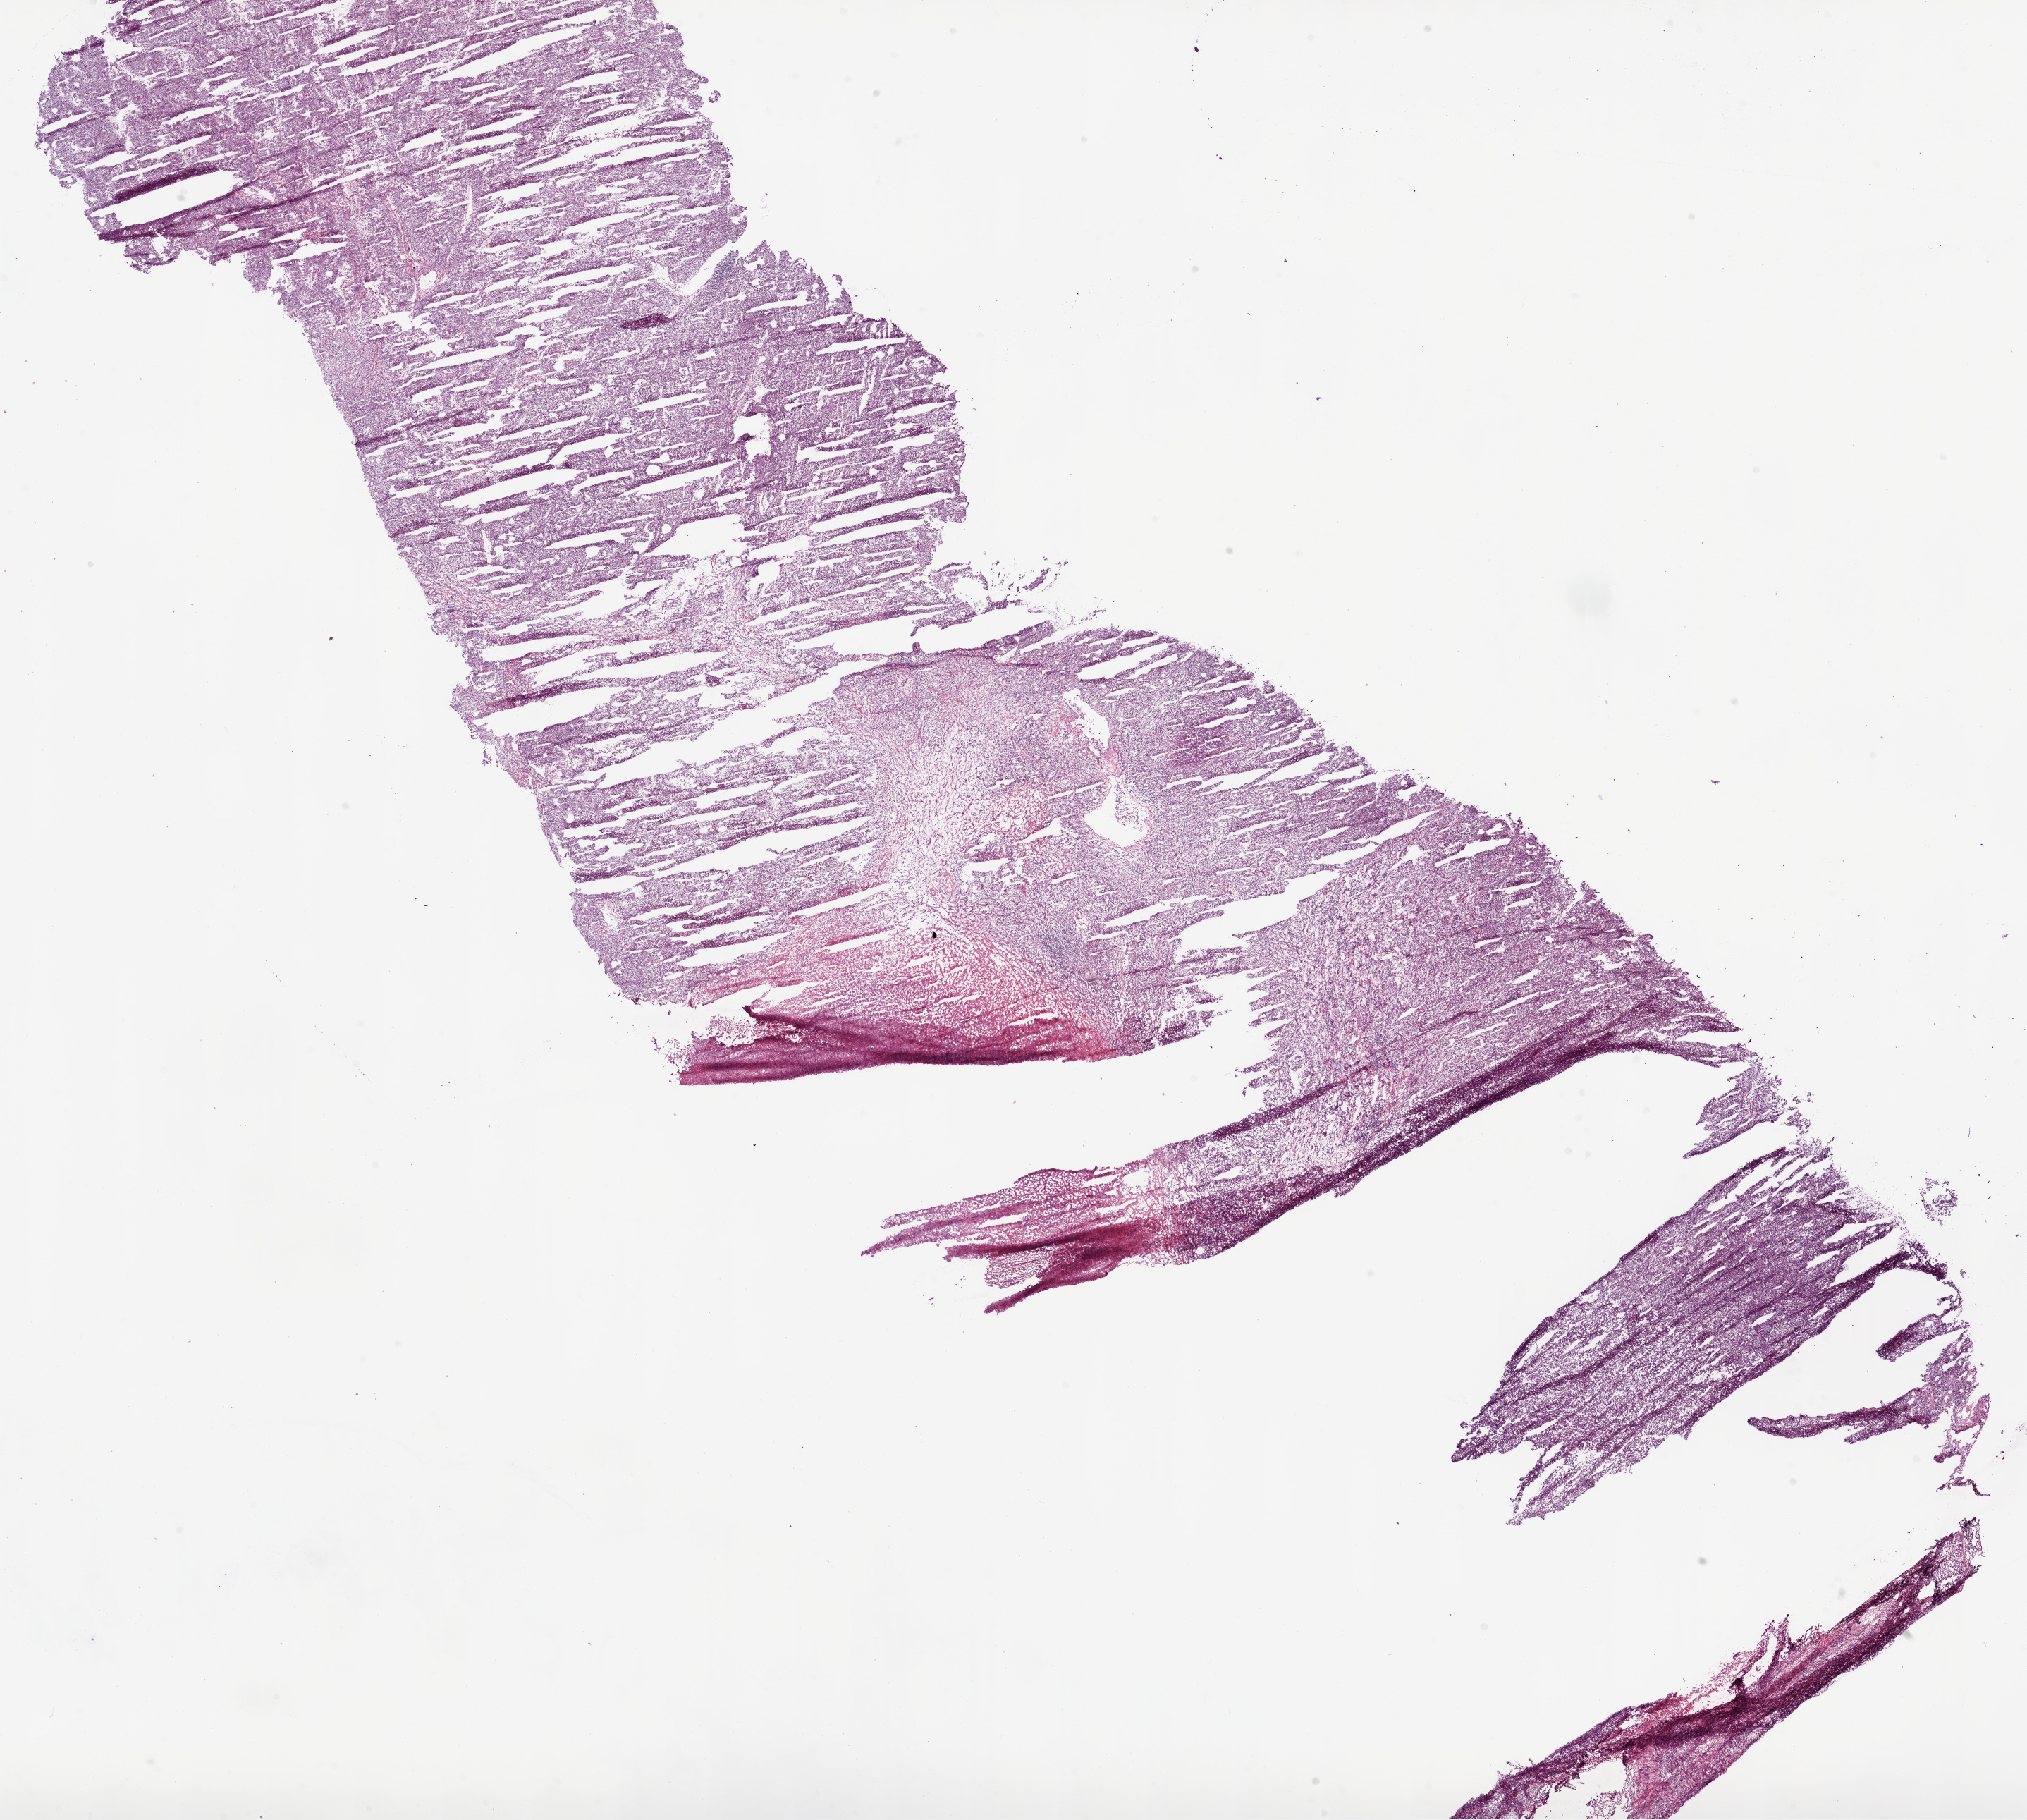
Whole-slide histology image, H&E, a low-resolution overview of the entire scanned area, about 23.1 x 20.7 mm; frozen section from the bottom of the tissue portion; sample: primary tumour, kidney. Male patient; age at initial diagnosis 81 years. Histologic grade: G3 (poorly differentiated). Slide review estimates, as recorded: tumour cells 85%, tumour nuclei 85%, normal cells 0%, stromal cells 5%, necrosis 10%.
* TNM: T3c N0 M0
* laterality: right
* diagnosis: Clear cell adenocarcinoma, NOS
* AJCC pathologic stage: III